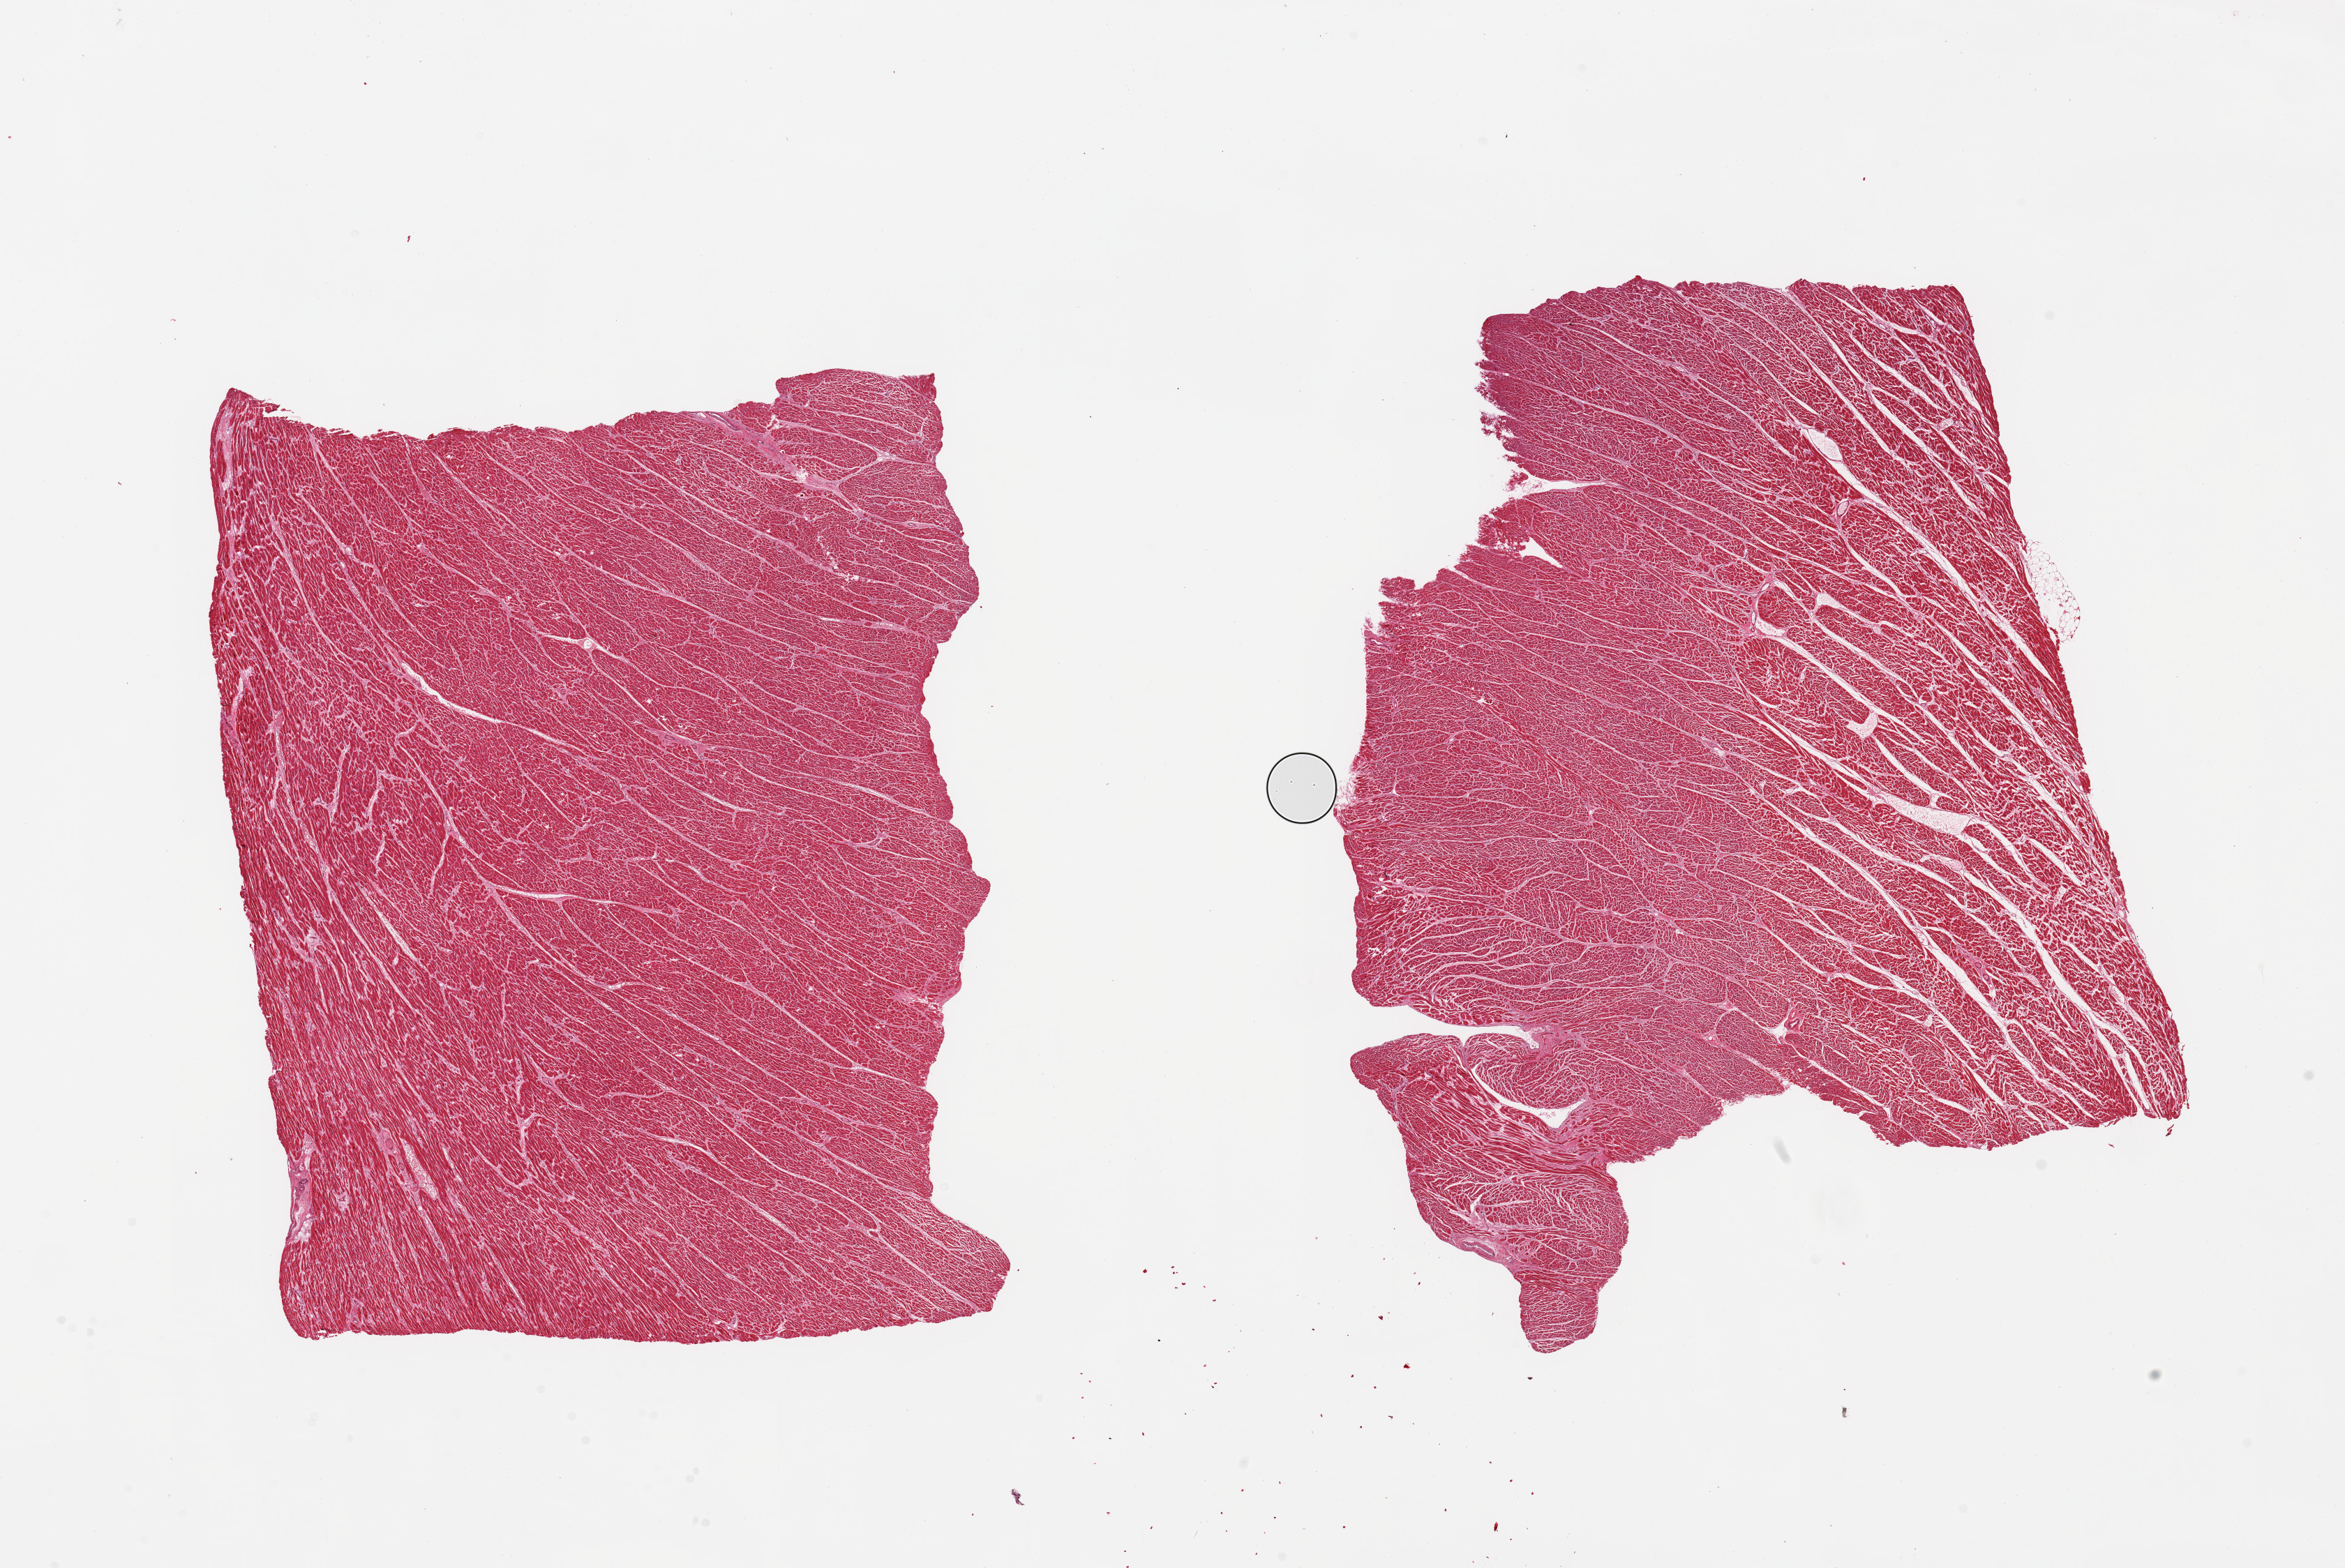
Haematoxylin and eosin whole-slide image, whole scanned area (about 26.6 x 17.8 mm) shown as a low-resolution overview. PAXgene-fixed, paraffin-embedded tissue. Target tissue: heart. Tissue donor sample.
Review note (as recorded): 2 pieces, minimal chronic ischemic changes/fibrosis.